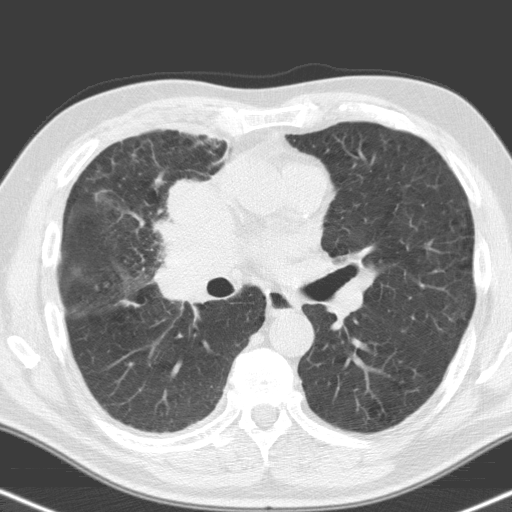
Low-dose screening chest CT, one axial slice; position 90 of 160 along the scan axis; lung window (W 1500 / L -600 HU); 512 × 512 image matrix, field of view 324 × 324 mm.
Annotated regions visible in this slice (outlined manually by an expert reader):
- lesion 1 (tumor, hilum of right lung): bounding box <159,180,239,305> (left, top, right, bottom; pixels)